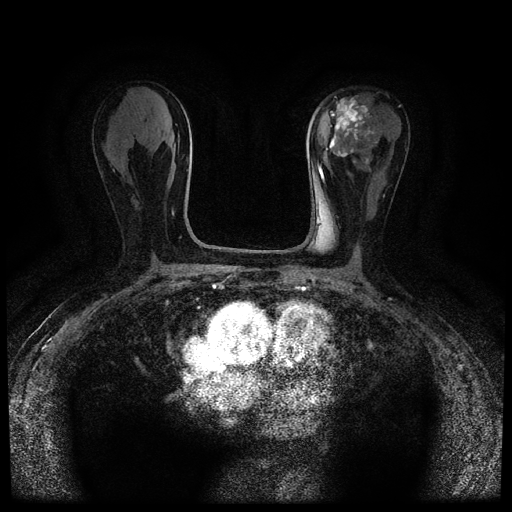
Breast MRI (dynamic contrast-enhanced, multi-phase), one axial slice. Dynamic contrast-enhanced series, time point 2 of 5 at this slice position (early post-contrast). 1.5 T. TE 2.7 ms, TR 5.4 ms. 2 mm slice thickness. 512 × 512 image matrix, field of view 320 × 320 mm. Patient: female, 80 years.
Annotated regions visible in this slice (semi-automatically segmented with operator editing):
- breast lesion (labelled 'tumour' in the annotation; benign lesions carry a separate 'benign' label): bounding box [x1, y1, x2, y2] px = [326, 96, 379, 169]